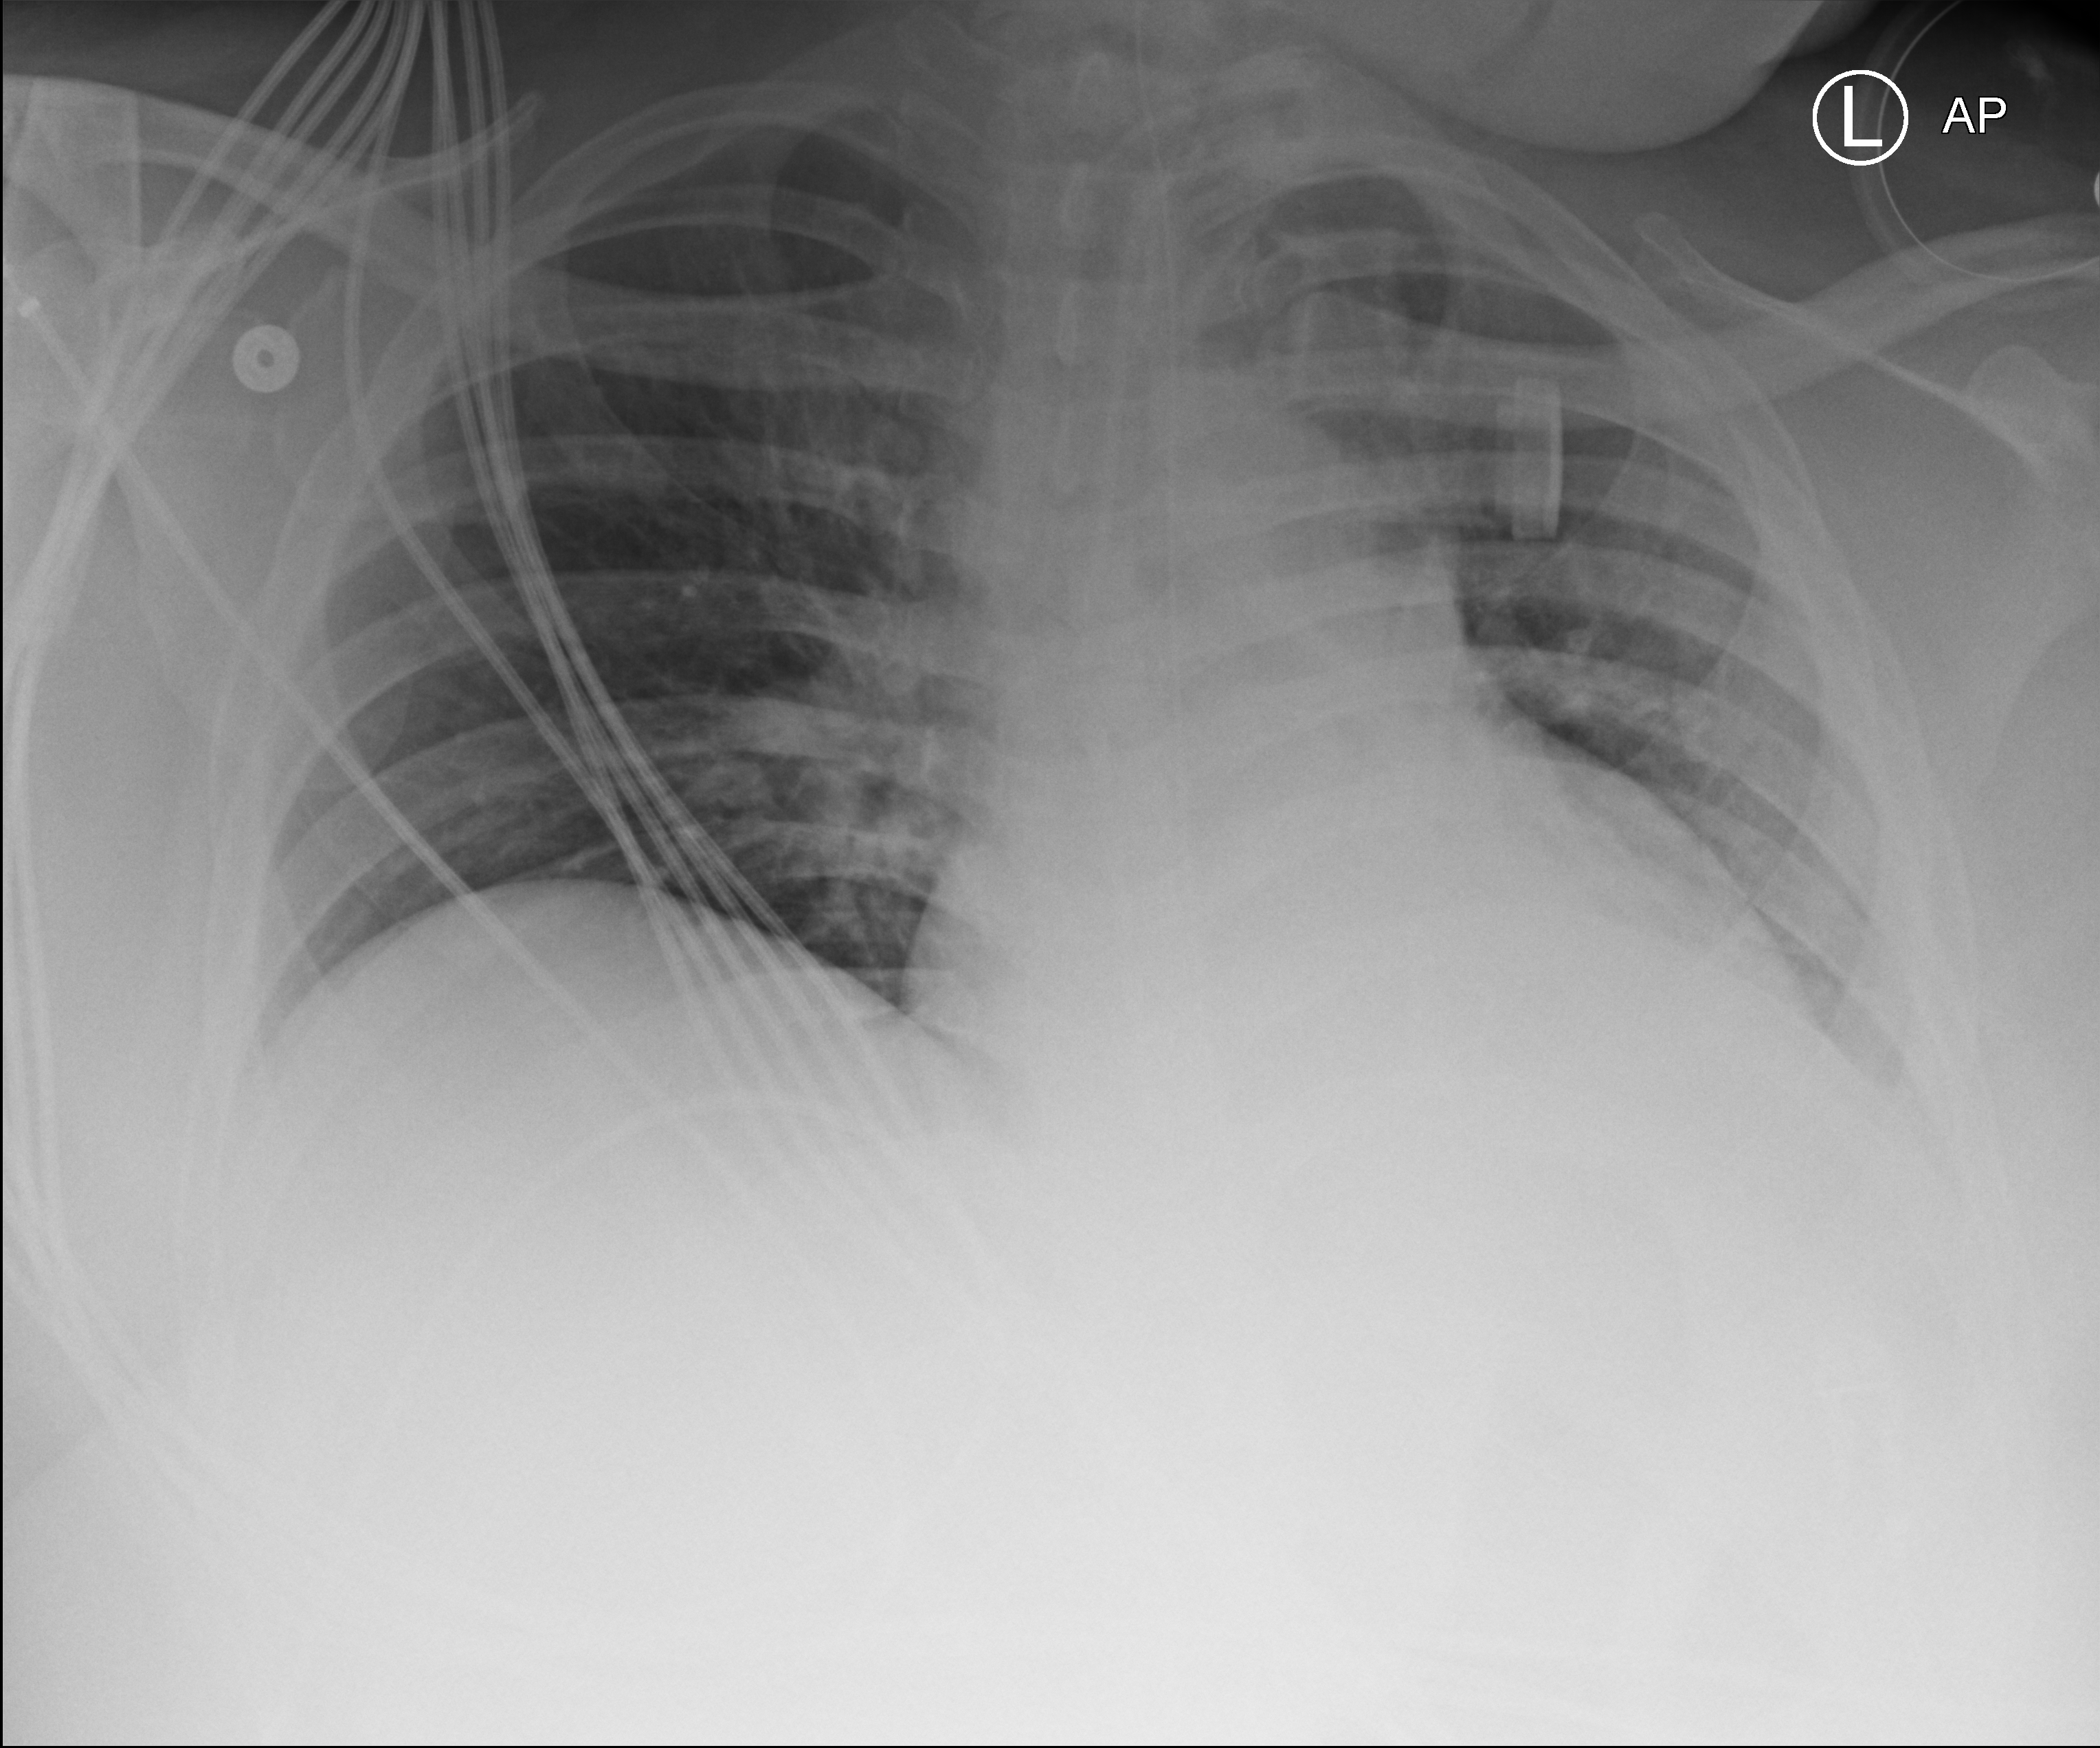
Chest X-ray (portable); anteroposterior (AP) projection. Patient hospitalised with COVID-19; male, aged 18–59 years.
From the hospital-stay record, not from the radiograph (when in the stay this image was taken is not recorded):
- chronic kidney disease (admission record): no
- admitted to intensive care during this hospital stay: yes
- mechanically ventilated during this hospital stay: yes